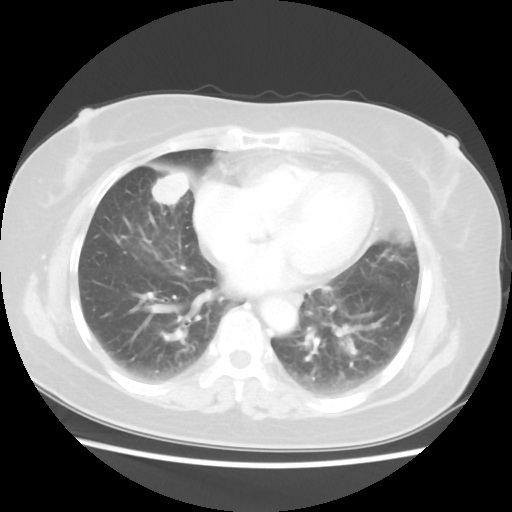
Chest CT, one axial slice. Position 20 of 48 along the scan axis. Lung window (W 1500 / L -600 HU). 5 mm slice thickness. 512 × 512 image matrix. Patient: female, 61 years. From the clinical record (not read from this slice): clinical TNM (as recorded): T1c N0 M0.
Outlined on this slice (bounding box drawn by a radiologist):
- lung tumour (recorded histology: adenocarcinoma): bounding box <148,168,190,209> (left, top, right, bottom; pixels)